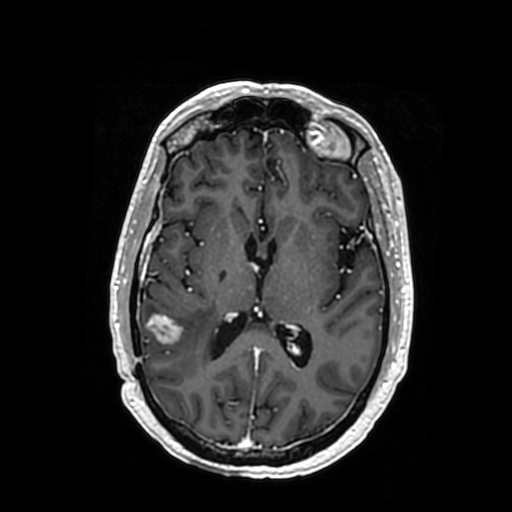
Brain MRI from a brain-tumour surgery series, one axial slice; position 175 of 364 along the scan axis; T1-weighted post-contrast; 0.5 mm slice thickness; 512 × 512 image matrix, field of view 260 × 260 mm. Case-level facts recorded for this patient, not image findings: histopathology: Oligodendroglioma; WHO grade: 3; IDH mutation: yes; tumour location: Right Posterior Temporal Inferior Parietal.
Outlined on this slice (outlined manually by an expert reader):
- tumour: bounding box (x1, y1, x2, y2) in pixels: (150, 315, 201, 372)